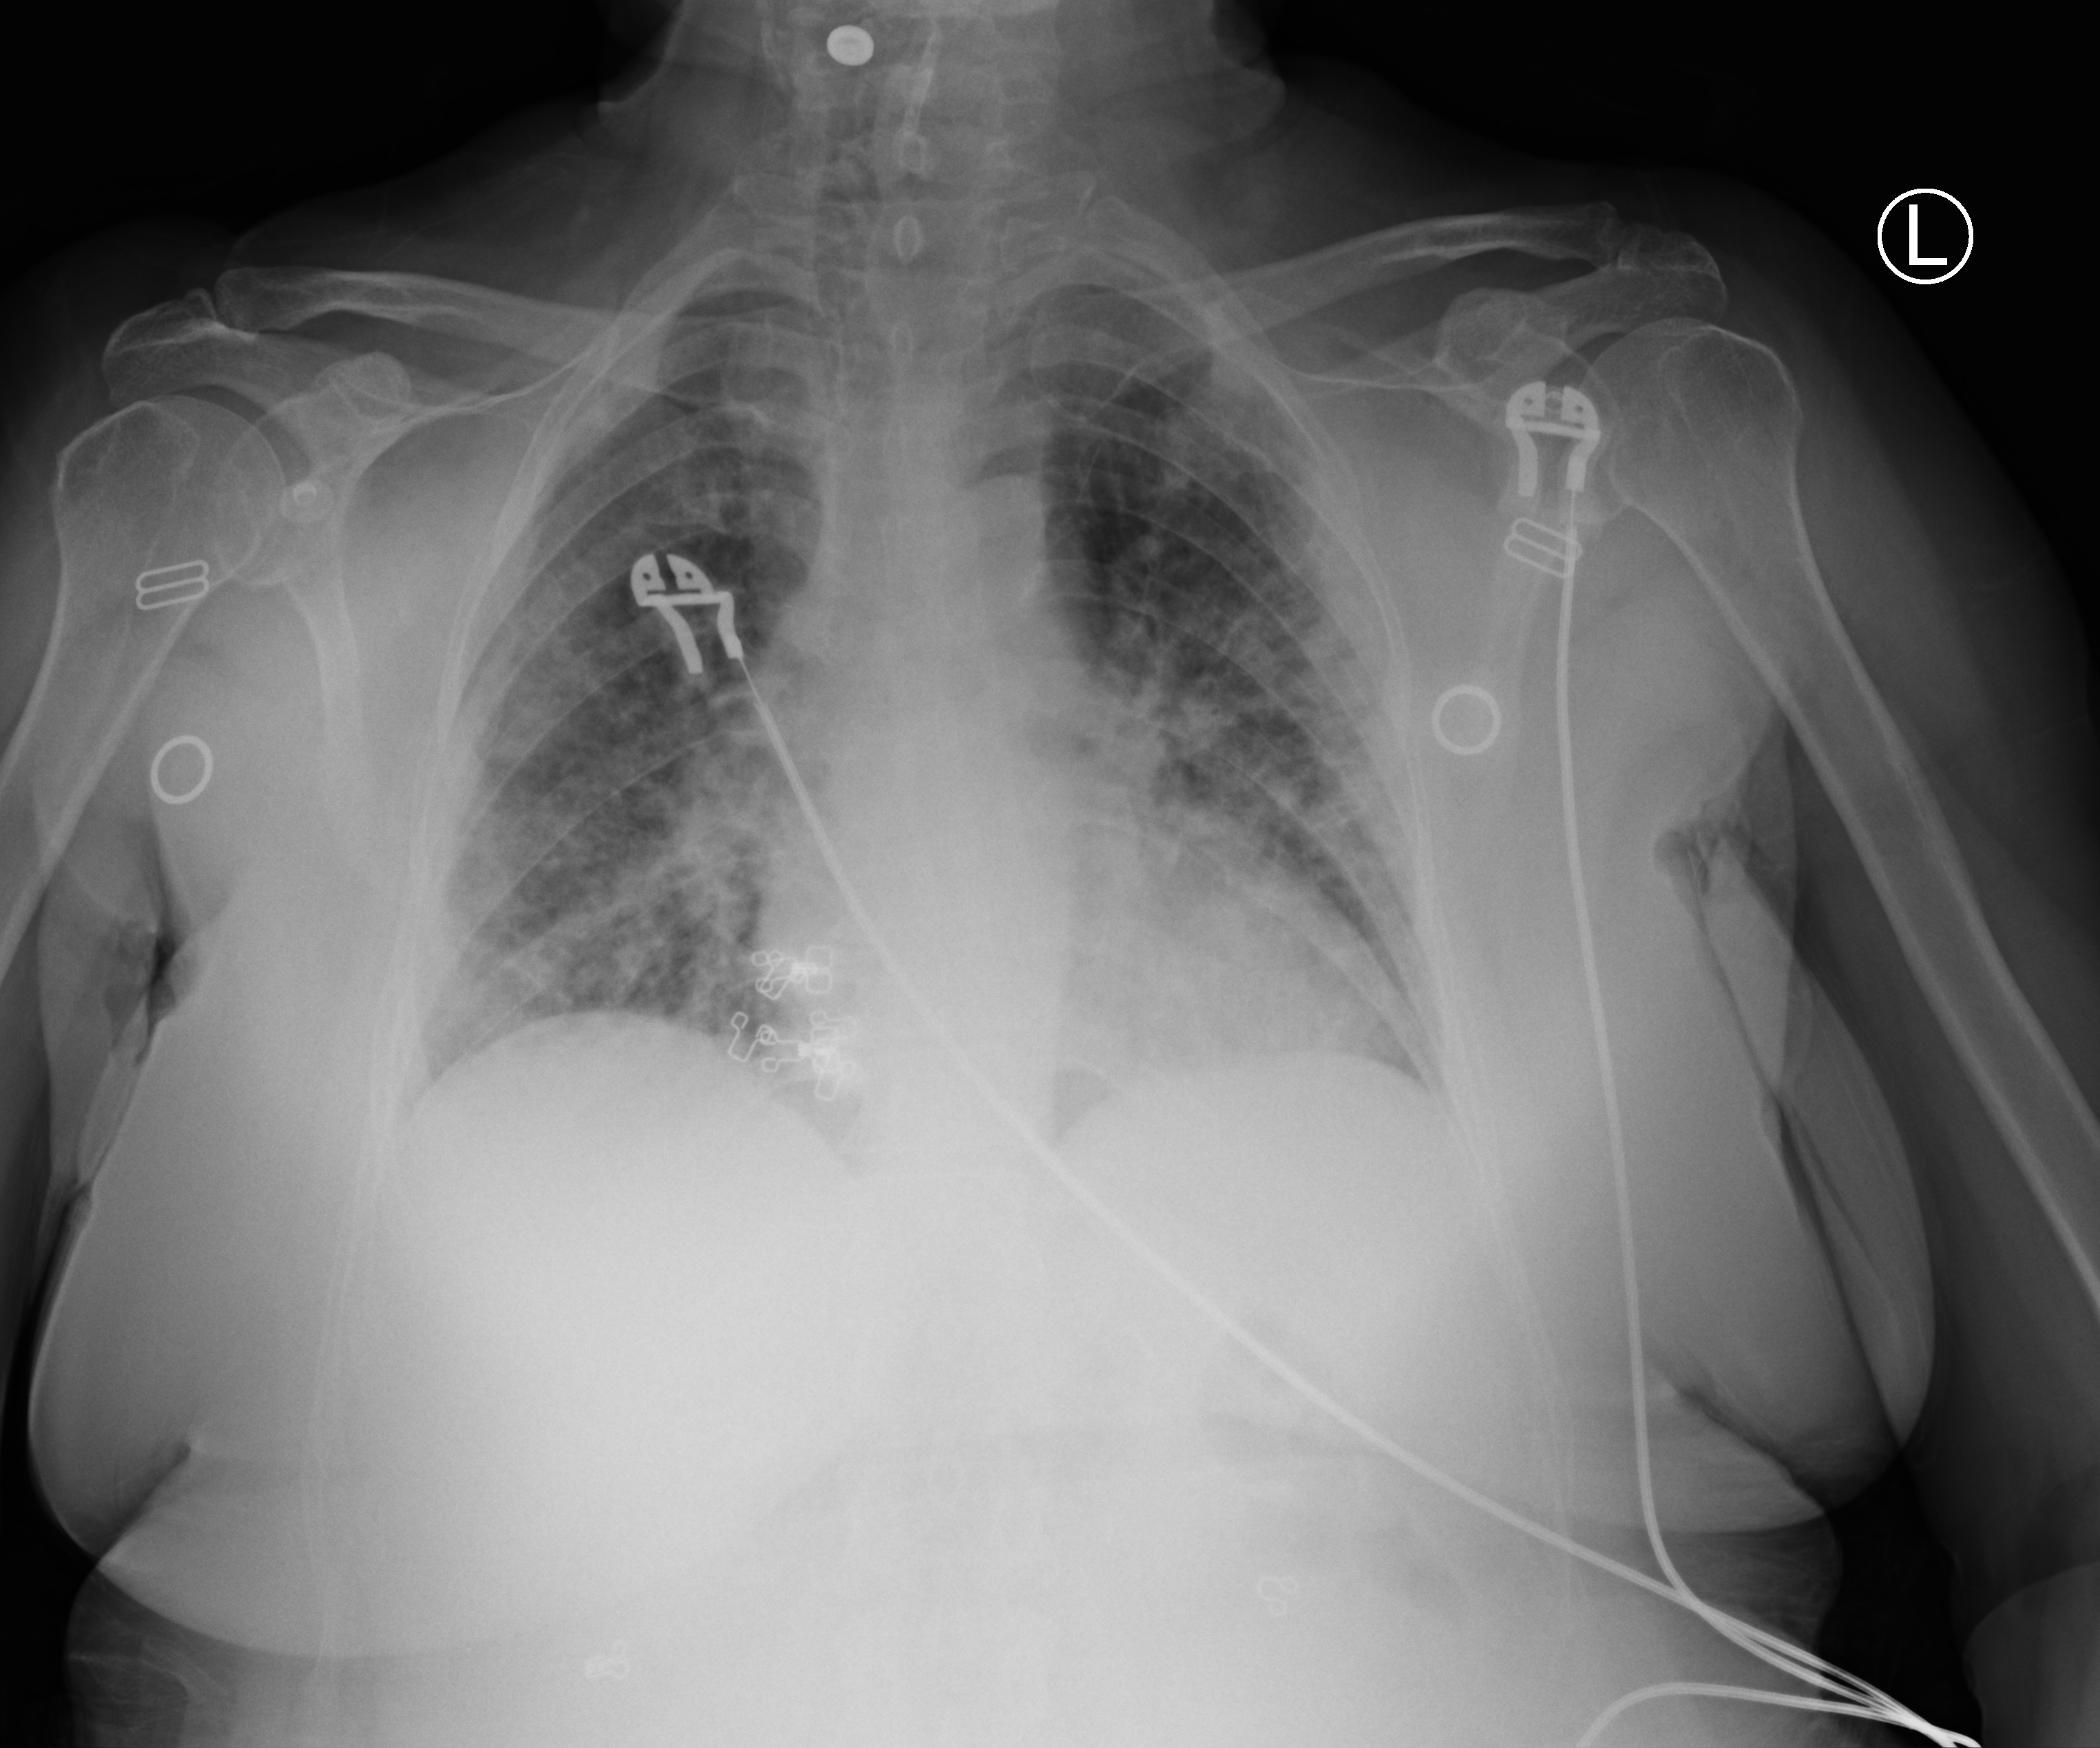
Chest X-ray (portable). Patient hospitalised with COVID-19; female, aged 60–74 years.
Admission-level facts for this patient (not findings on this image; timing relative to this image not recorded): length of hospital stay: 2 days; COPD (admission record): no.